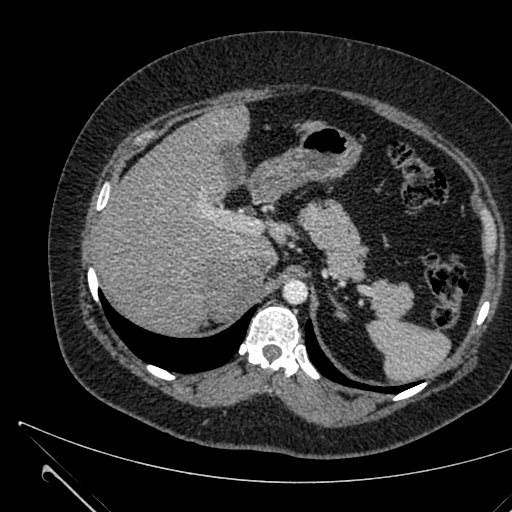
Contrast-enhanced abdominal CT, one axial slice; slice 469 of 731 in the series (ordered by position); 120 kVp; intravenous contrast given; soft-tissue window (W 400 / L 40 HU); 1 mm slice thickness; 512 × 512 image matrix, field of view 376 × 376 mm. Female patient, age 36 years. Case-level facts recorded for this patient, not image findings: diagnosis: adrenocortical carcinoma; tumour side: right adrenal; tumour size at pathology: 10 cm; Ki-67 index: 20 %; stage (as recorded): 4.
Outlined on this slice (semi-automatically segmented with operator editing):
- mass: bounding box <206,258,261,322> (left, top, right, bottom; pixels)